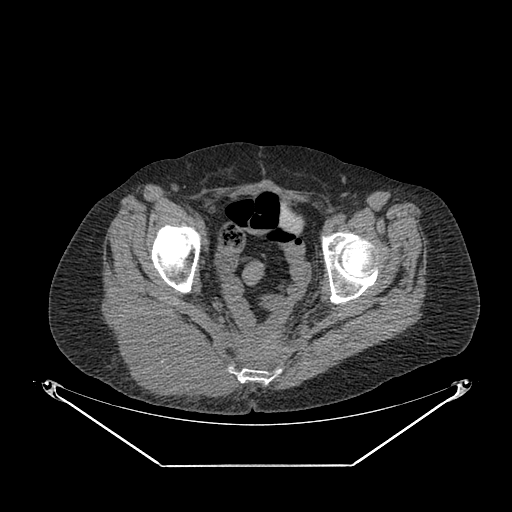
CT of an extremity soft-tissue mass (from a PET/CT study), one axial slice. Position 59 of 267 along the scan axis. Reconstruction kernel SOFT. 140 kVp. Soft-tissue window (W 400 / L 40 HU). 3.75 mm slice thickness. 512 × 512 image matrix, field of view 500 × 500 mm. Female patient. Case-level facts recorded for this patient, not image findings: histological type: spindle cell suggestive of myxofibrosarcoma; grade: intermediate; site of the primary tumour: right buttock.
Annotated regions visible in this slice (expert contour drawn on MRI and transferred to this co-registered scan by the dataset authors):
- gross tumour volume (mass): bounding box [x1, y1, x2, y2] px = [112, 315, 225, 401]